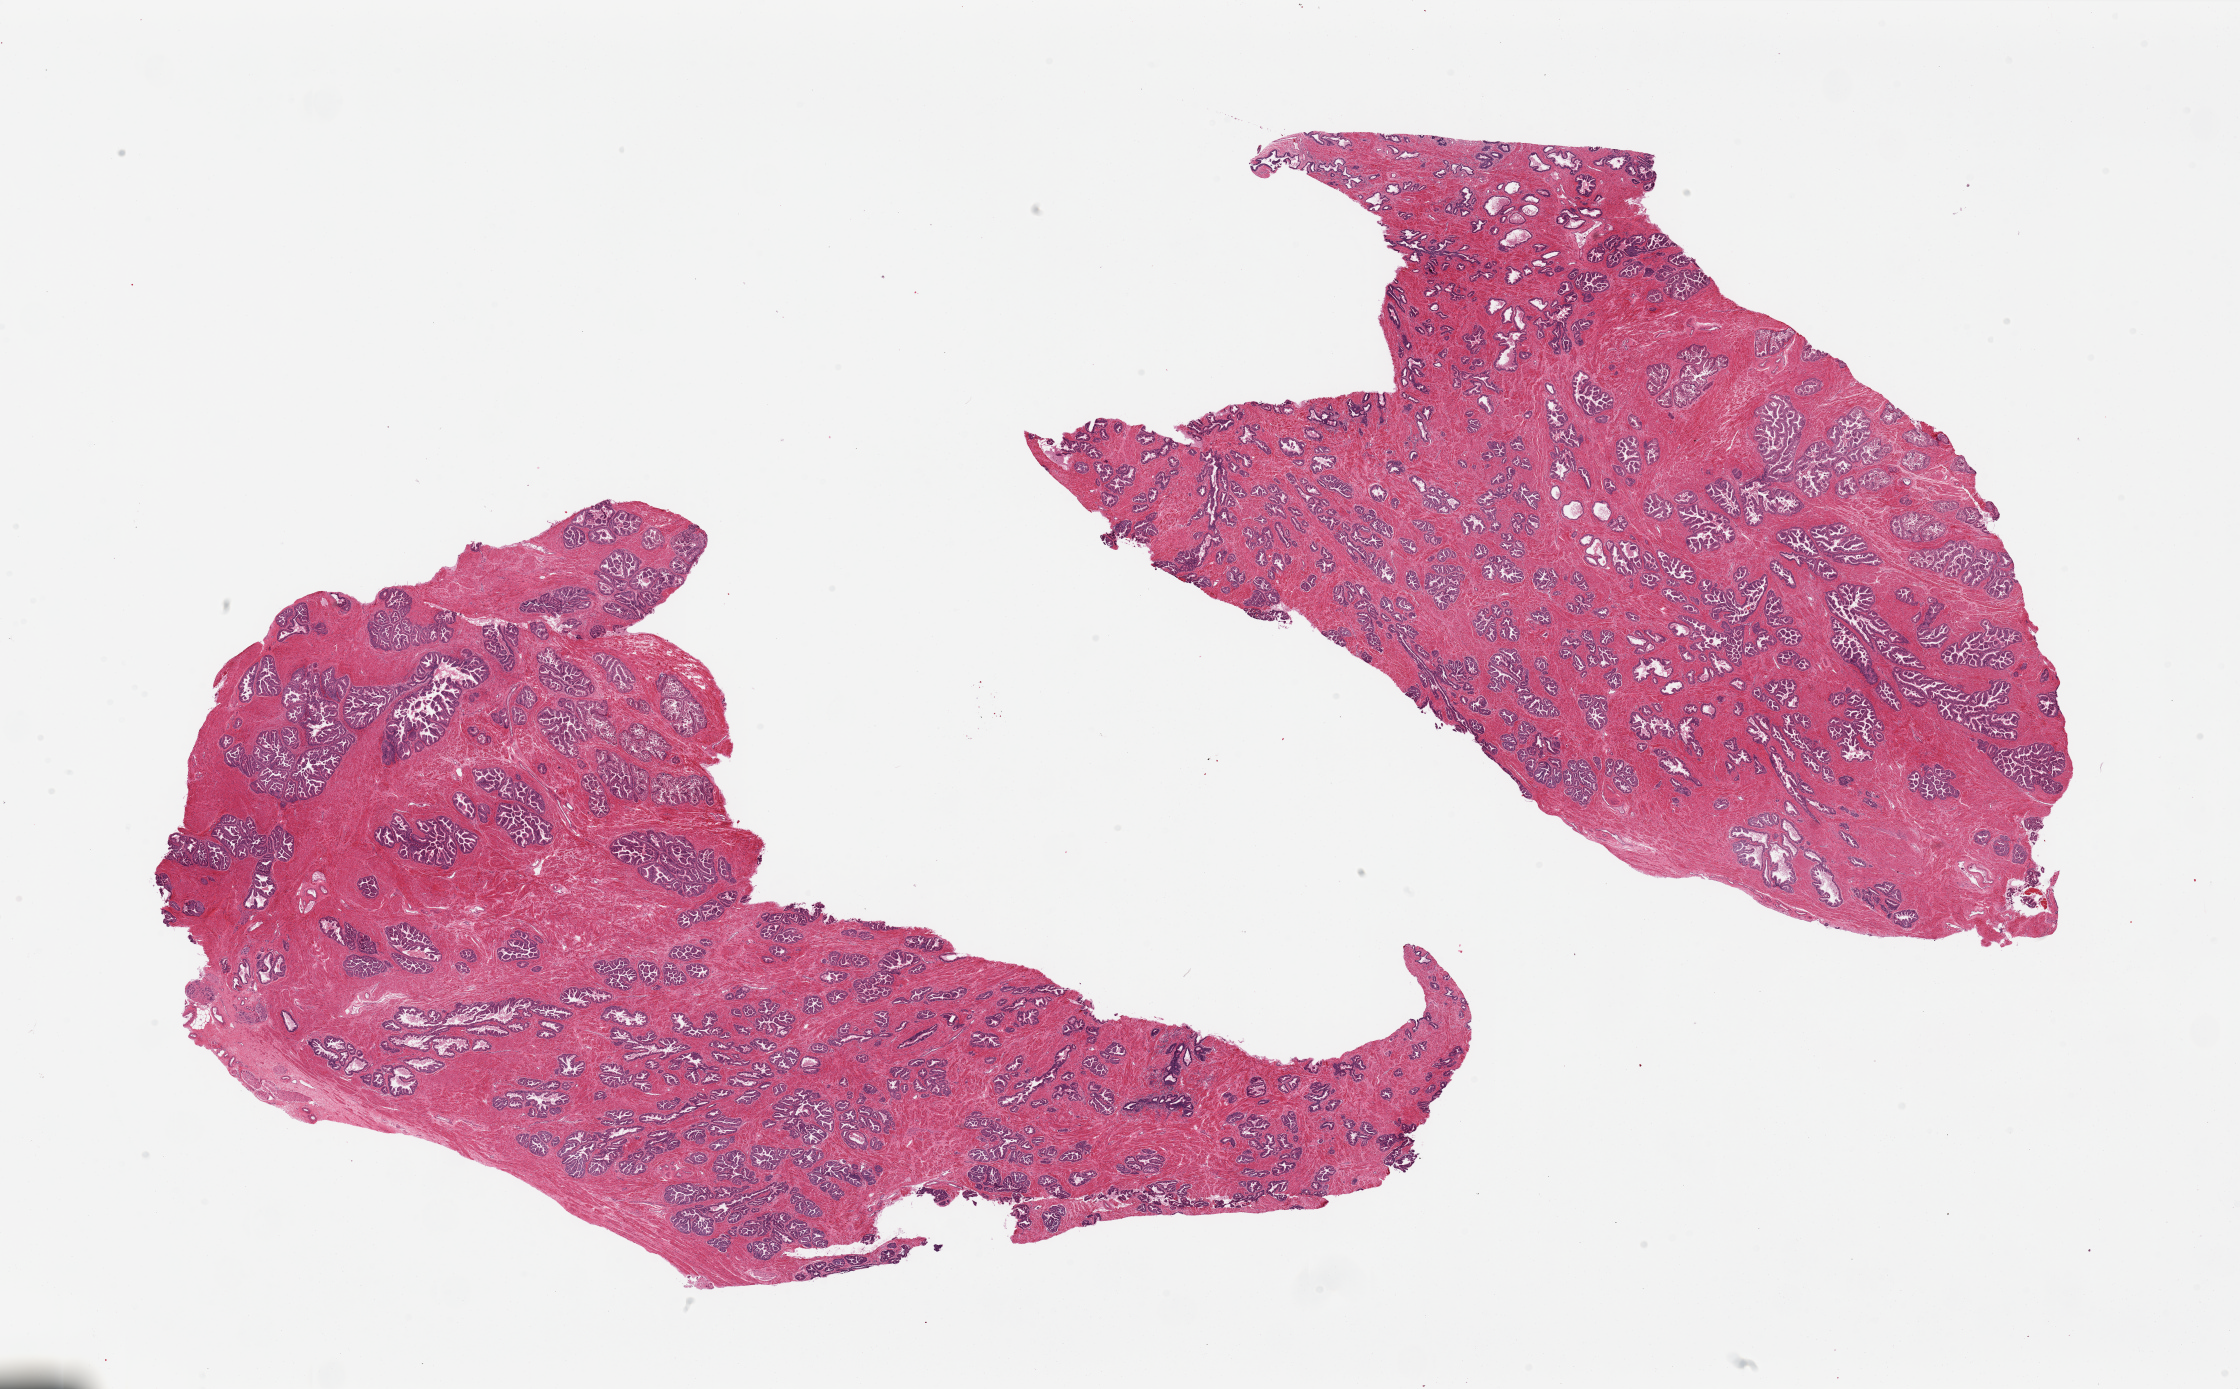
Whole-slide image, hematoxylin and eosin (H&E) stain, brightfield, a low-resolution overview of the entire scanned area, about 35.4 x 22.0 mm (acquisition: 20x scan). PAXgene-fixed, paraffin-embedded tissue. Sampled site (target tissue): prostate. Donor tissue sample.
Review note (as recorded): 2 pieces, epithelium focally sloughing.